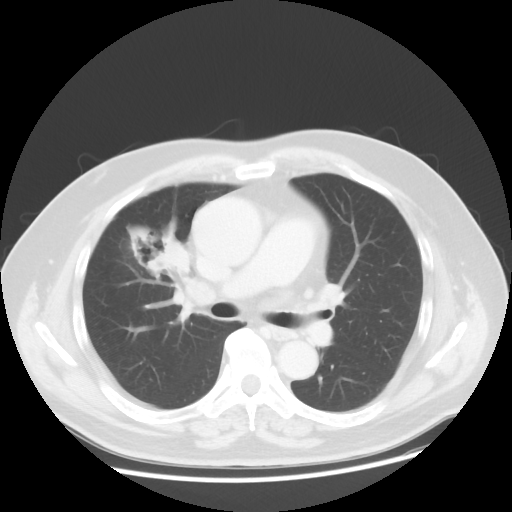
Chest CT, one axial slice. Position 26 of 48 along the scan axis. 120 kVp. Lung window (W 1500 / L -600 HU). 512 × 512 image matrix. Male patient, age 60 years. From the clinical record (not read from this slice): clinical TNM (as recorded): T2 N3 M0; histopathological grade: G2-3.
Structures marked on this image (rectangle marked by the reading radiologist):
- lung tumour (recorded histology: adenocarcinoma): bounding box (x1, y1, x2, y2) in pixels: (118, 206, 191, 286)